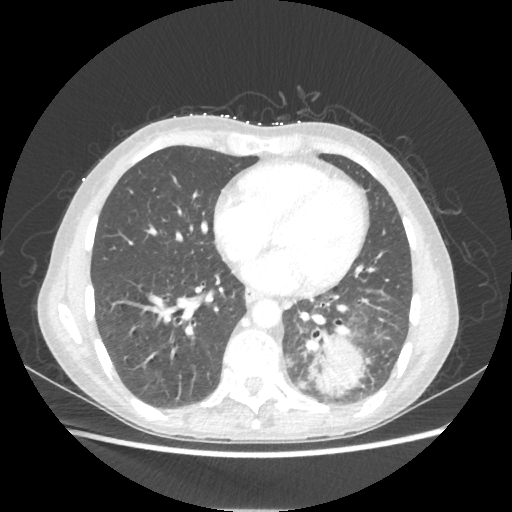
Chest CT, one axial slice. Position 87 of 221 along the scan axis. Lung window (W 1500 / L -600 HU). 1.25 mm slice thickness. 512 × 512 image matrix, field of view 360 × 360 mm. Female patient, age 53 years. Case-level facts recorded for this patient, not image findings: clinical TNM (as recorded): T3 N0 M0.
Annotated regions visible in this slice (rectangle marked by the reading radiologist):
- lung tumour (recorded histology: adenocarcinoma): bounding box (x1, y1, x2, y2) in pixels: (308, 332, 364, 398)